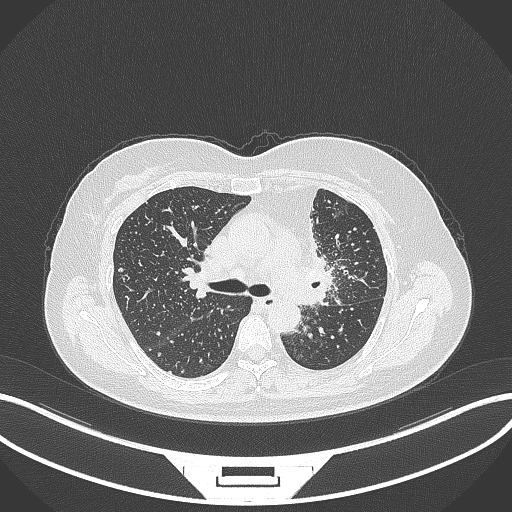
Chest CT, one axial slice. Slice 212 of 348 in the series (ordered by position). Reconstruction kernel B70f. Lung window (W 1500 / L -600 HU). 1 mm slice thickness. 512 × 512 image matrix, field of view 400 × 400 mm. Female patient, age 49 years. From the clinical record (not read from this slice): clinical TNM (as recorded): T1c N0 M1.
Structures marked on this image (bounding box drawn by a radiologist):
- lung tumour (recorded histology: adenocarcinoma): bounding box <293,242,336,307> (left, top, right, bottom; pixels)